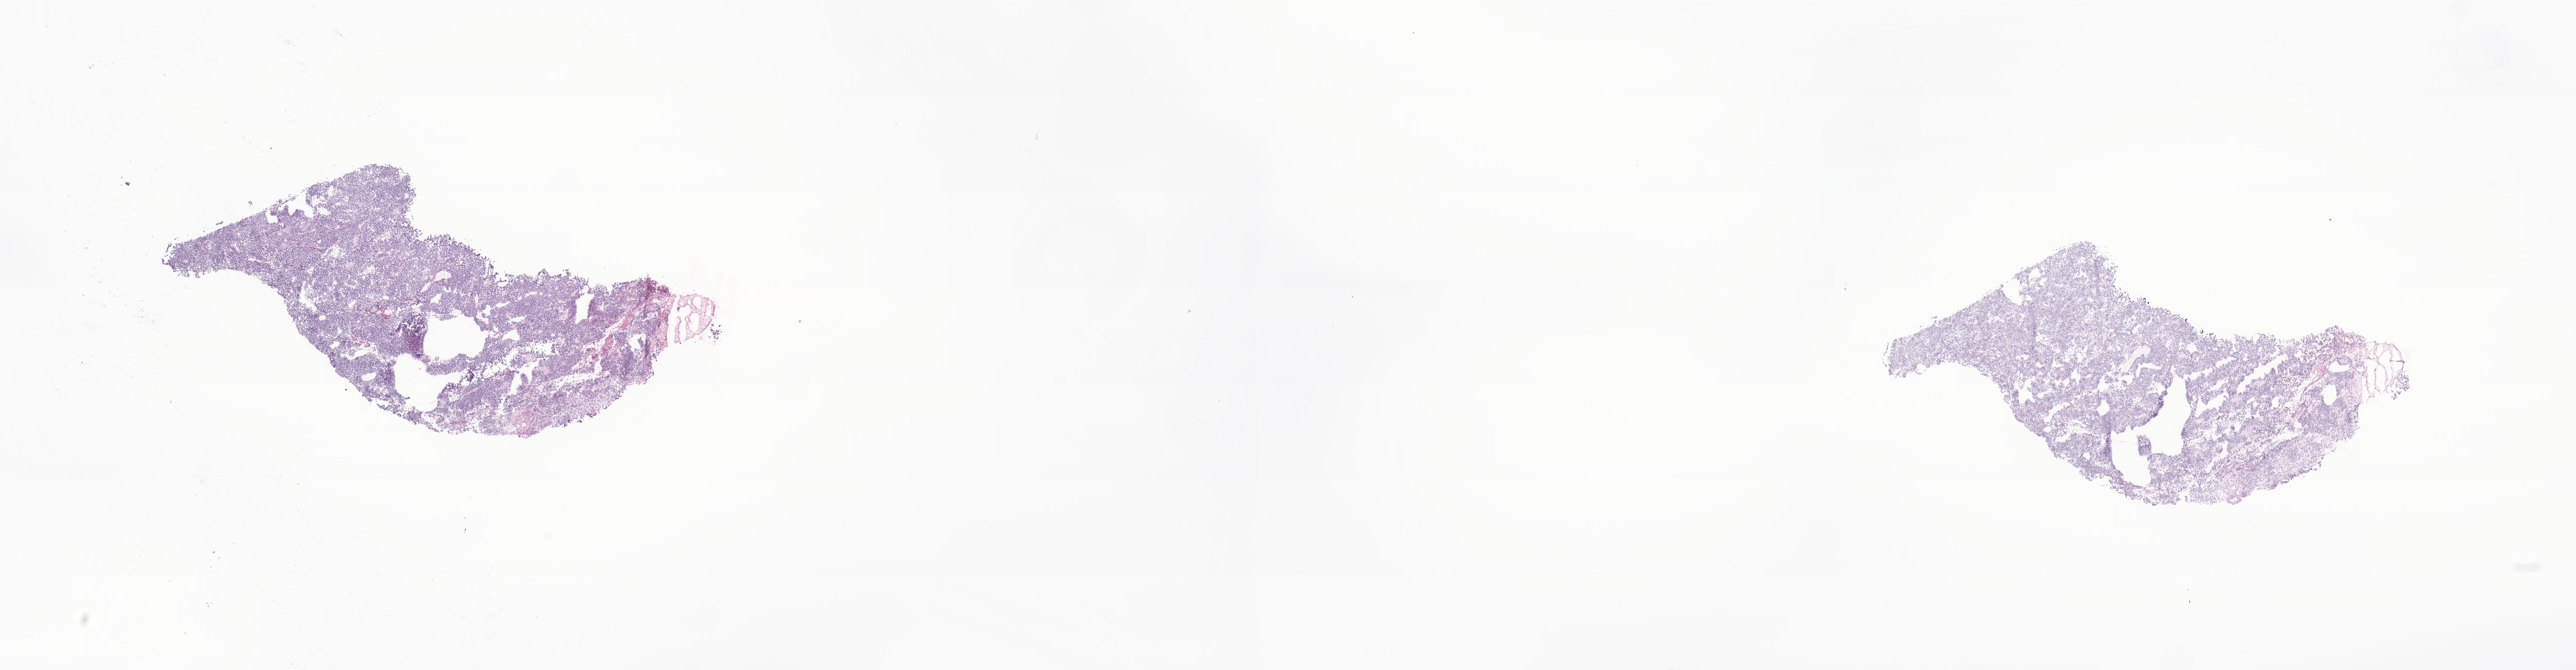
Whole-slide image, H&E stain of tumor tissue from the brain, whole scanned area (about 28.8 x 7.5 mm) shown as a low-resolution overview. Frozen section (OCT-embedded). Patient male; age 33 months (2 years 9 months).
Diagnosis: Medulloblastoma, NOS.